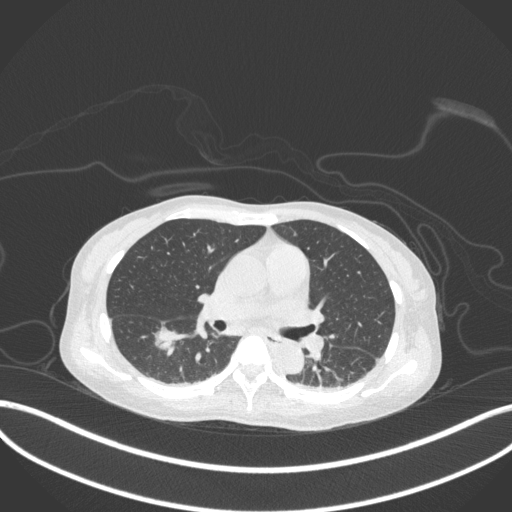
Chest CT, one axial slice; slice 171 of 260 in the series (ordered by position); 120 kVp; lung window (W 1500 / L -600 HU); 512 × 512 image matrix, field of view 400 × 400 mm. Patient: female, 44 years. Case-level facts recorded for this patient, not image findings: clinical TNM (as recorded): T1c N0 M0.
Outlined on this slice (bounding box drawn by a radiologist):
- lung tumour (recorded histology: adenocarcinoma): bounding box <147,316,187,361> (left, top, right, bottom; pixels)